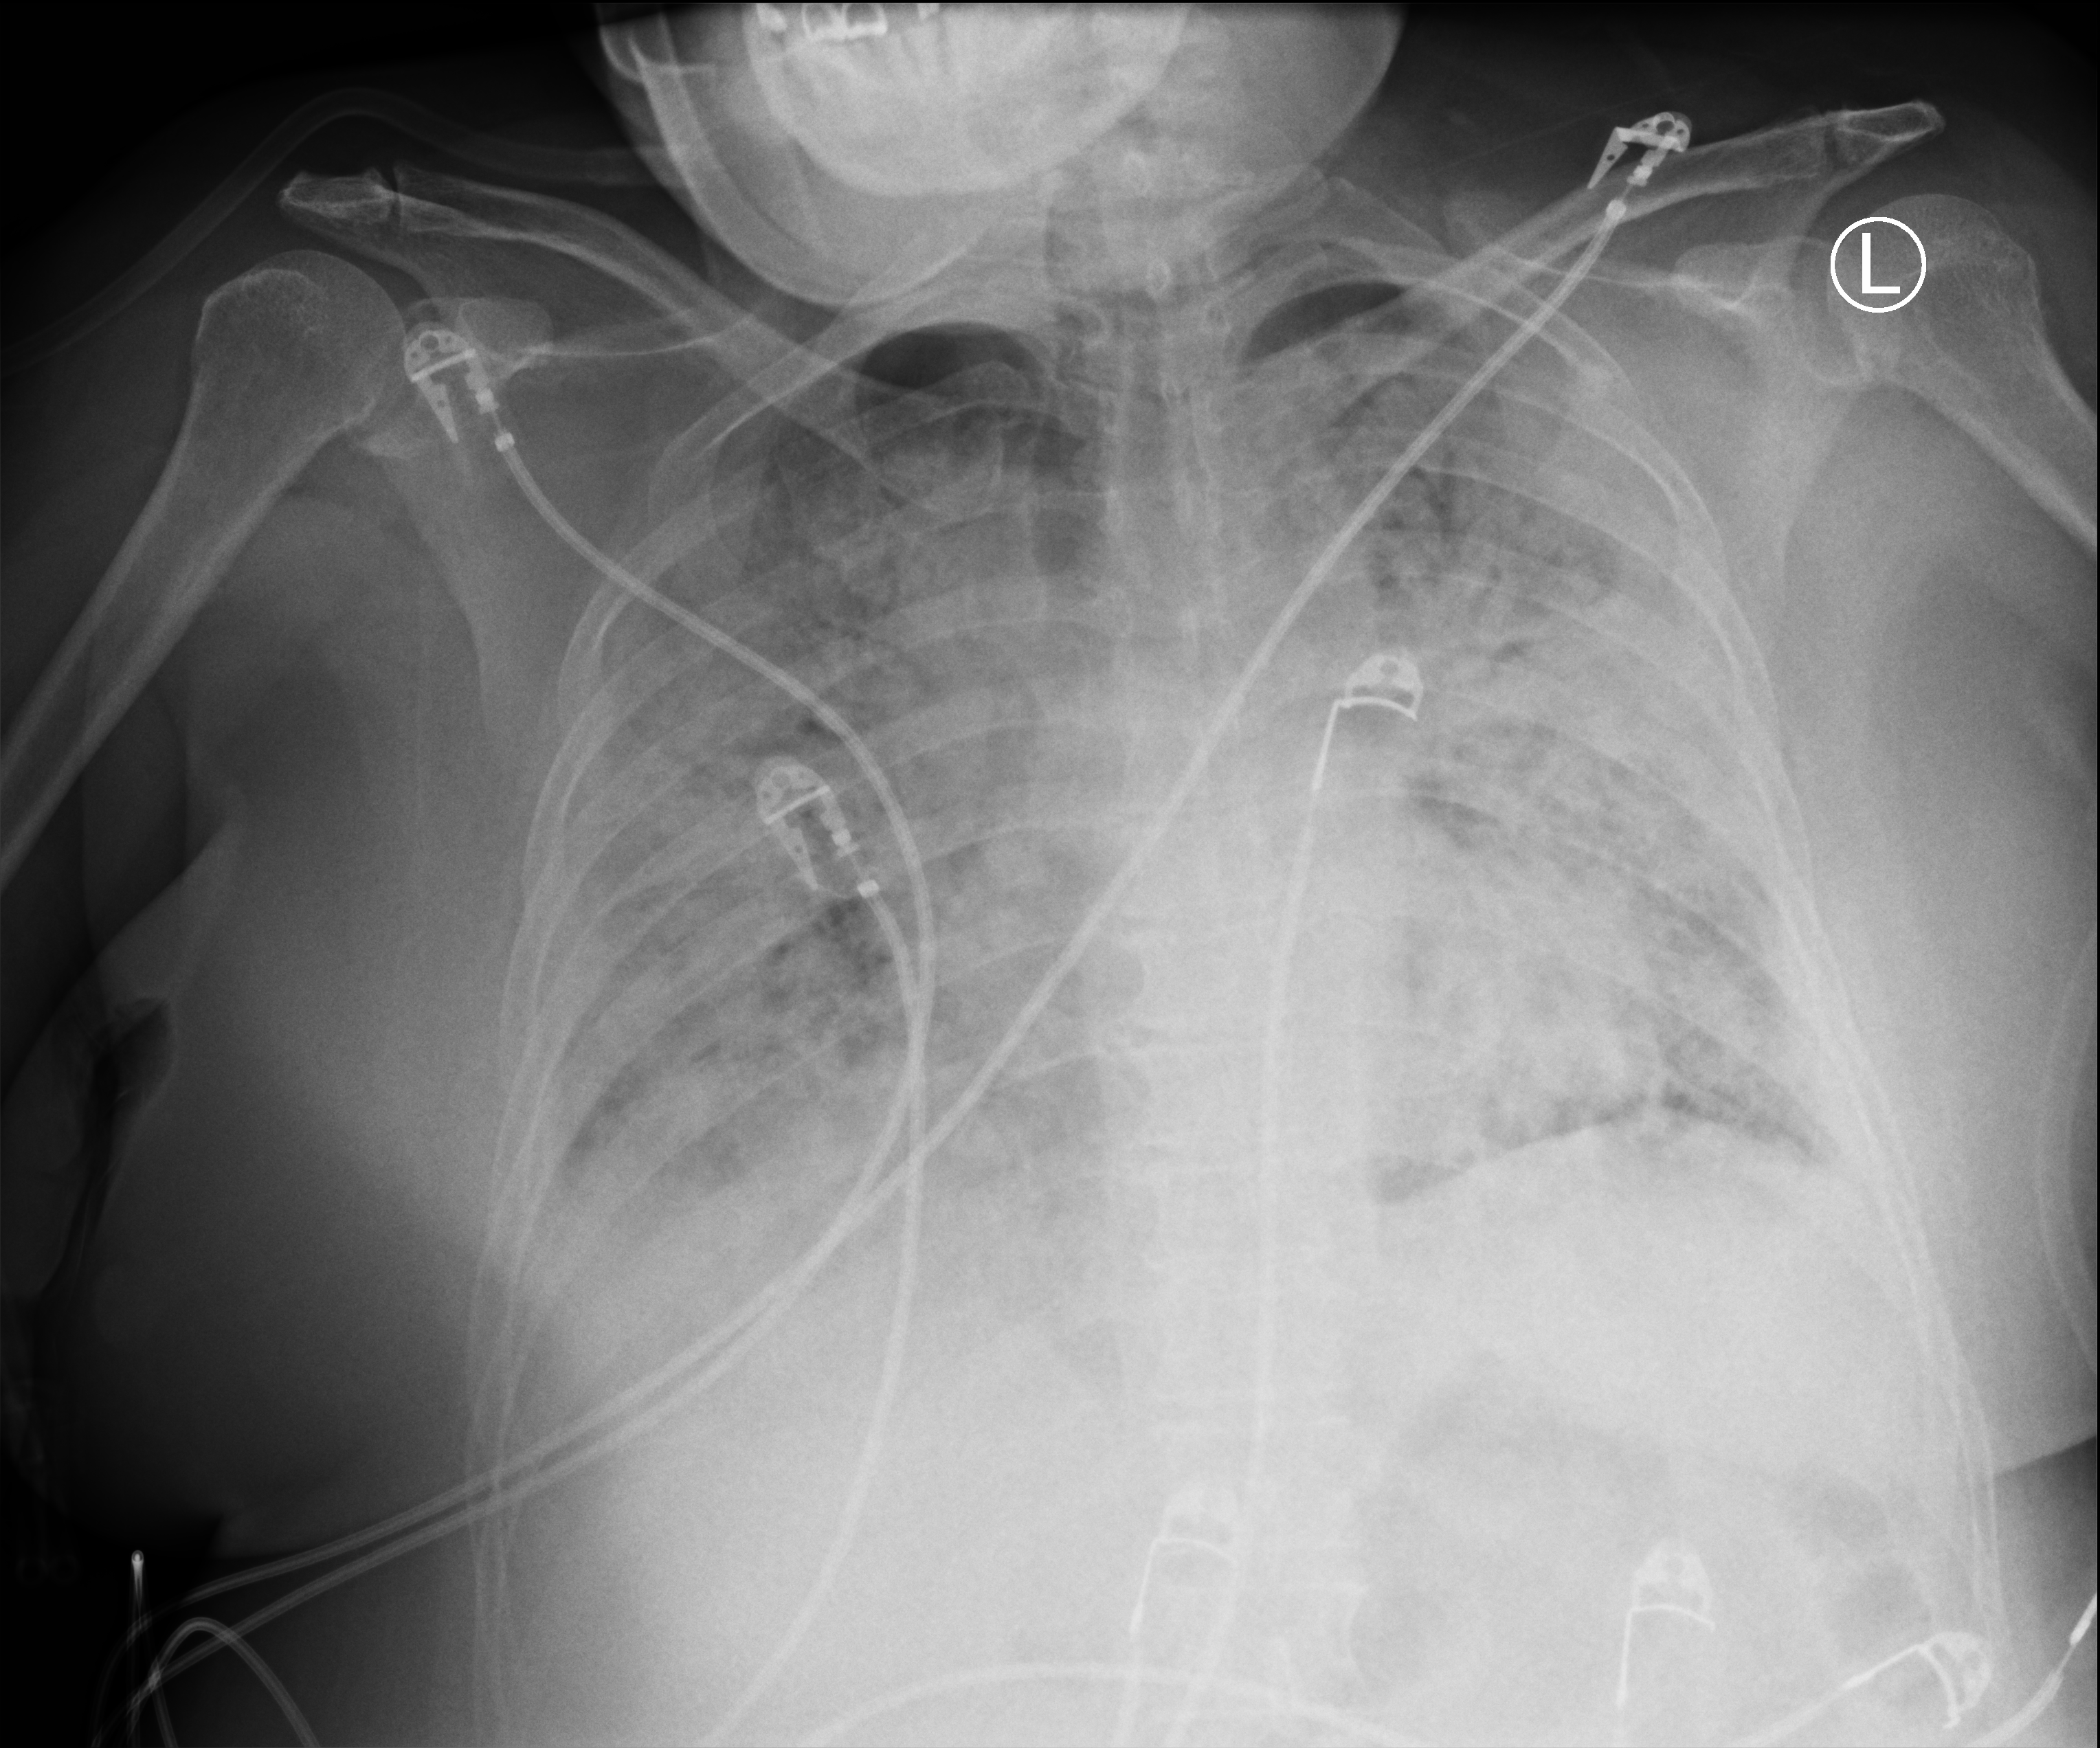
Chest X-ray (portable). Female patient hospitalised with COVID-19, age 18–59 years.
Hospital-stay facts (about this admission, not read from this image; timing relative to this image not recorded): hypertension (admission record): no; admitted to intensive care during this hospital stay: no.